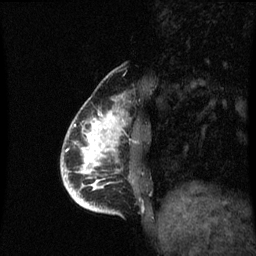
Breast MRI (dynamic contrast-enhanced), one sagittal slice. Slice 18 of 60 in the series (ordered by position). Dynamic contrast-enhanced series, image 2 of 3 at this slice position (ordered by acquisition). 1.5 T. TE 4.2 ms, TR 8.9 ms. 2 mm slice thickness. 256 × 256 image matrix, field of view 200 × 200 mm. Female patient, age 35 years. Case-level facts recorded for this patient, not image findings: setting: breast cancer imaged before/during neoadjuvant chemotherapy; receptor status: HR-positive, HER2-negative.
Structures marked on this image (semi-automatic segmentation, software-assisted and operator-edited):
- analysis volume of interest (the breast-tissue region the enhancement analysis was run in; not a lesion): box from (x=66, y=102) to (x=133, y=213) px
- tumour enhancement mask (voxels above the 70 % enhancement threshold inside the analysis volume of interest): (x=77, y=114)–(x=120, y=211)